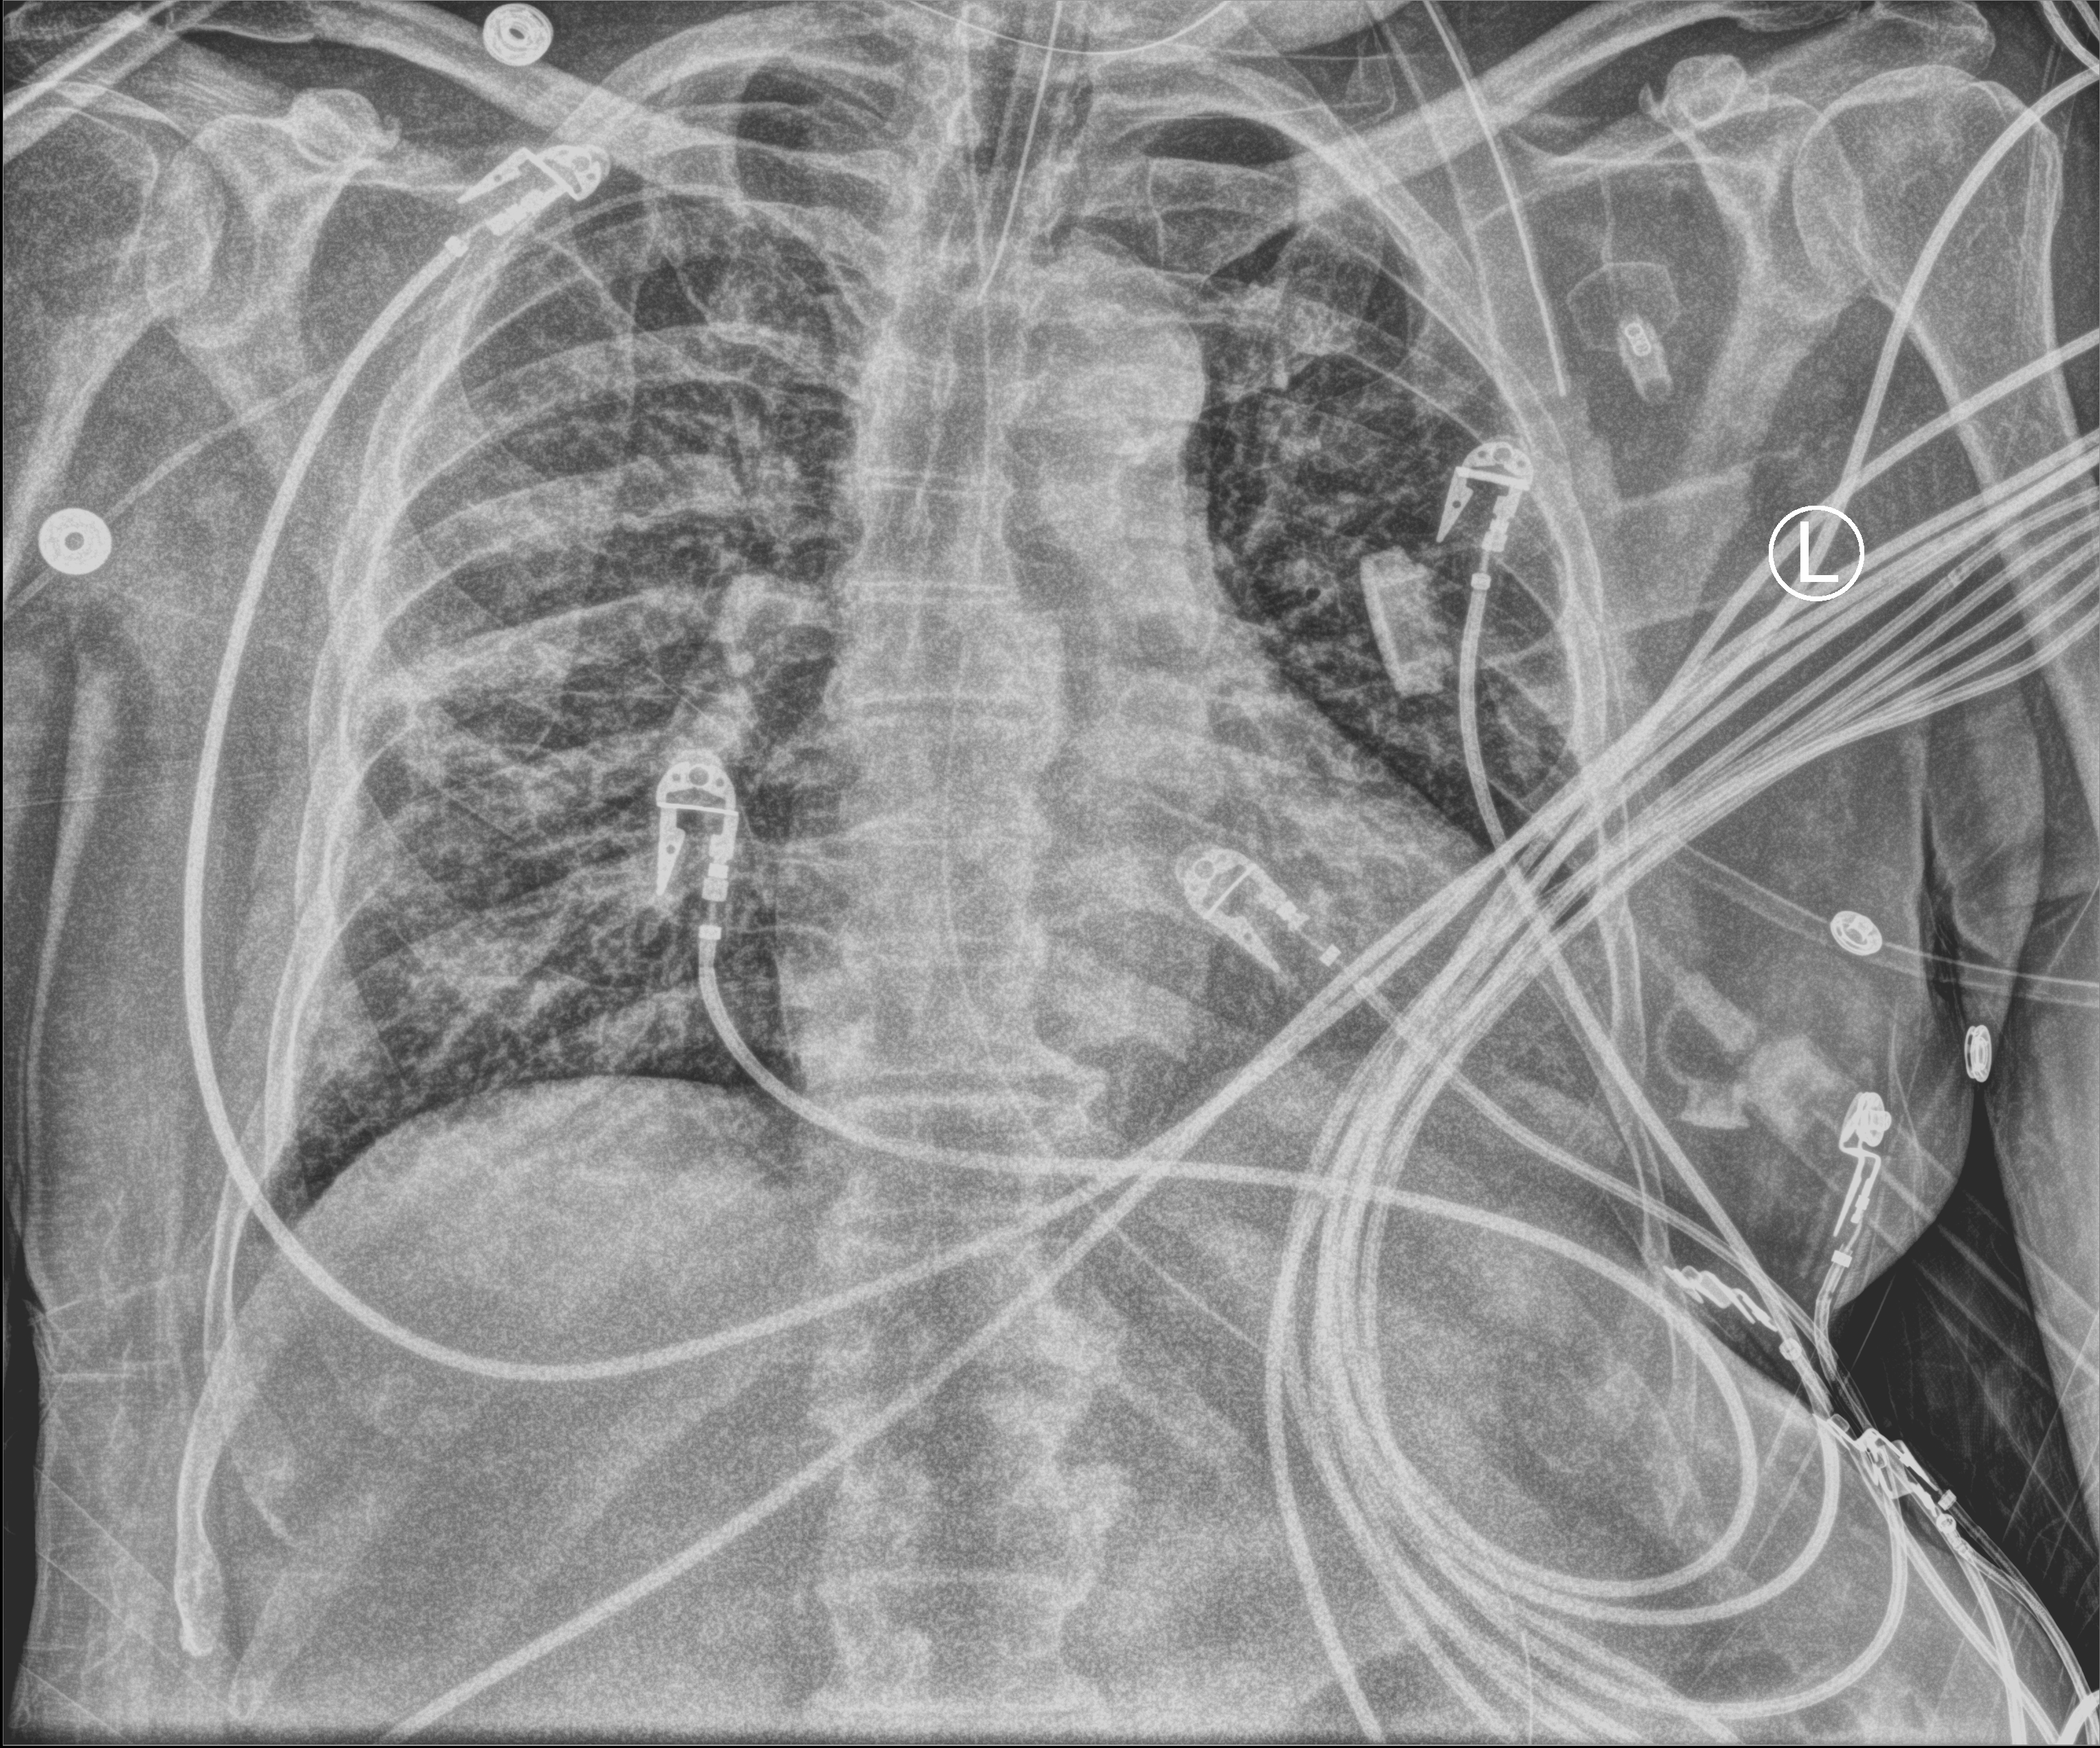
Chest X-ray (portable); anteroposterior (AP) projection. Male patient hospitalised with COVID-19, age 60–74 years.
Hospital-stay facts (about this admission, not read from this image; timing relative to this image not recorded):
- mechanically ventilated during this hospital stay: yes
- length of hospital stay: 31 days
- chronic kidney disease (admission record): no